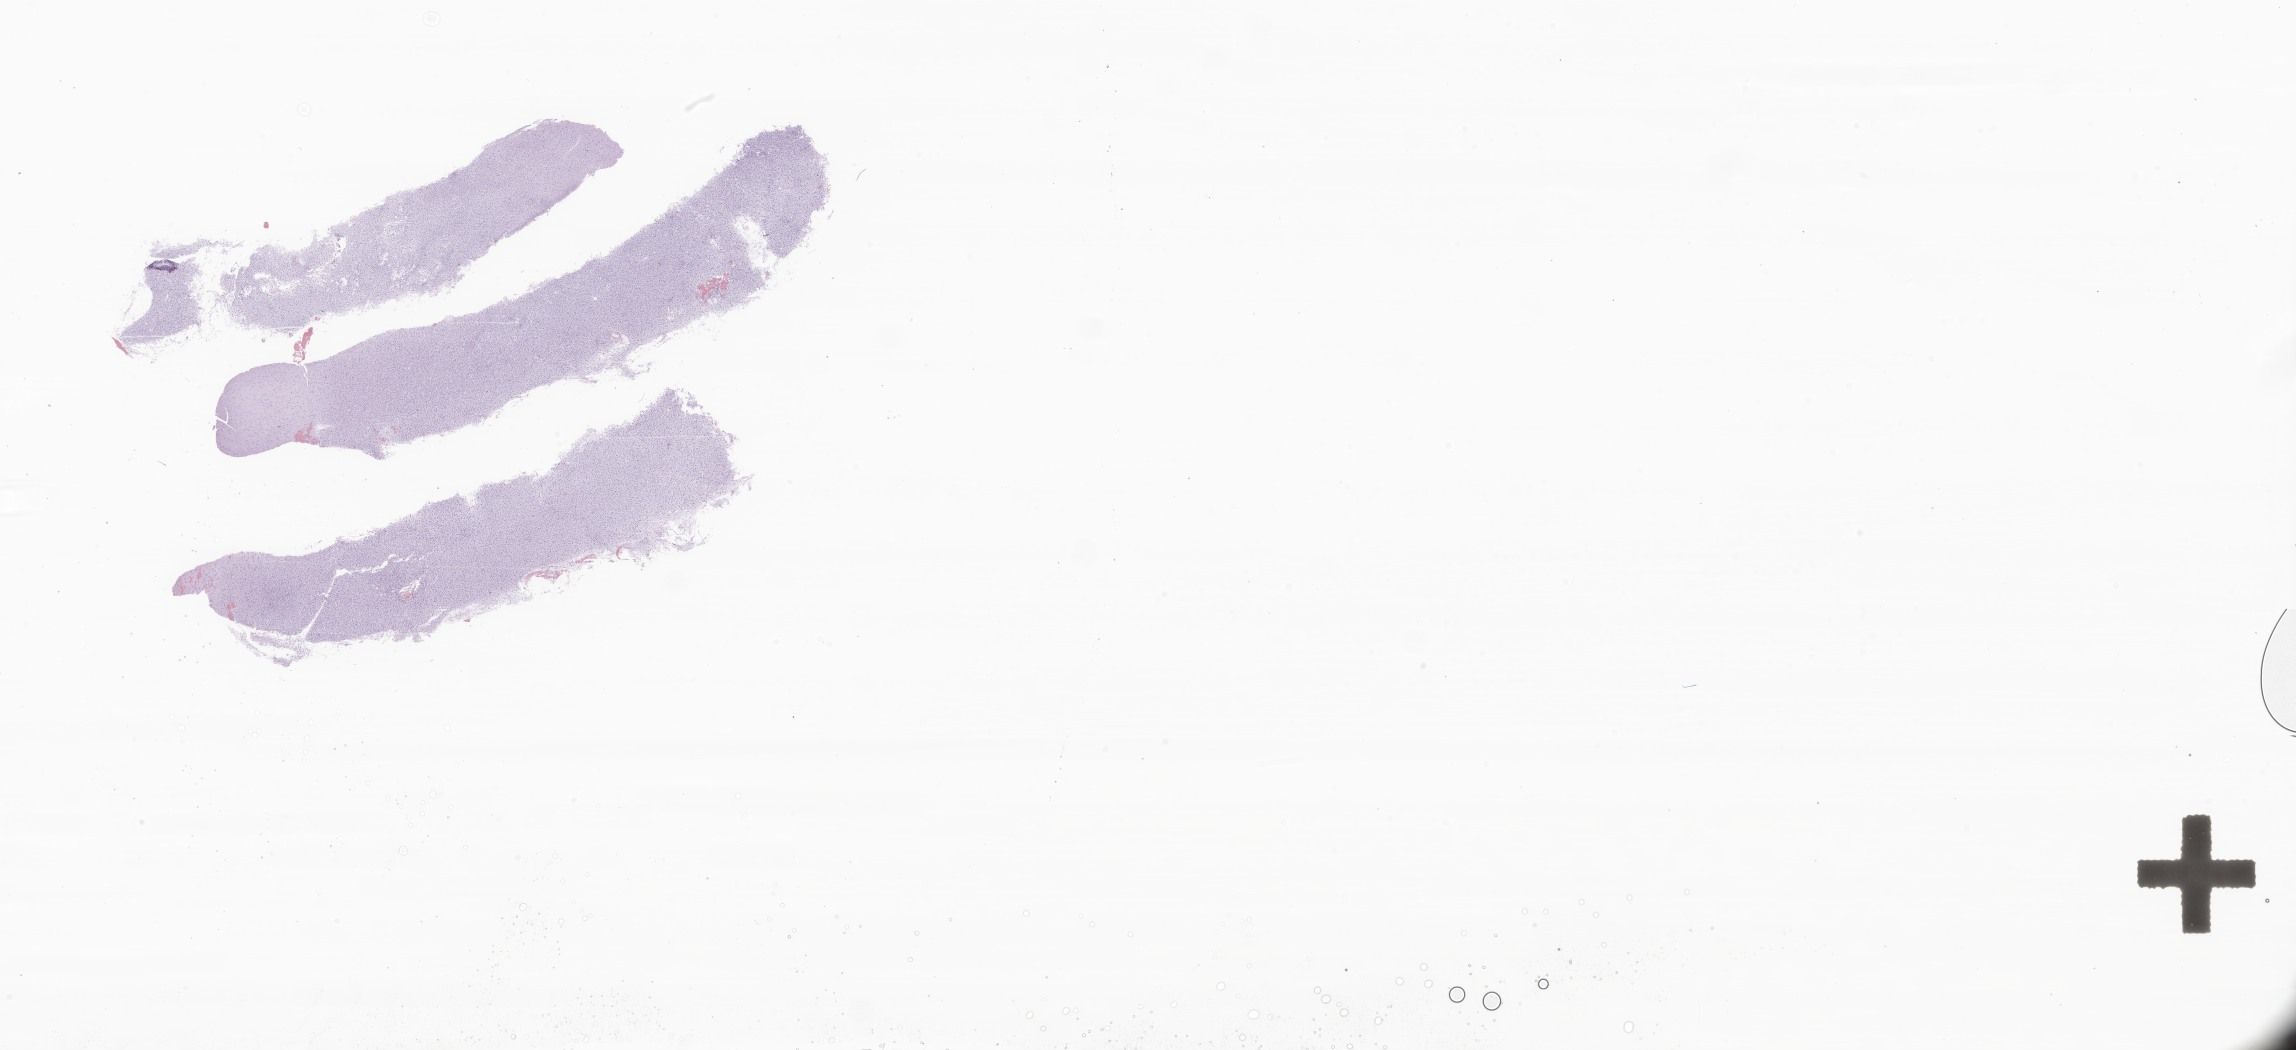
Digitized haematoxylin and eosin-stained section of tumor tissue from the brain, a low-resolution overview of the entire scanned area, about 38.7 x 17.7 mm; FFPE section. Female patient, age 182 months (15 years 2 months).
* diagnosis (ICD-O-3 morphology term): Oligodendroglioma, NOS